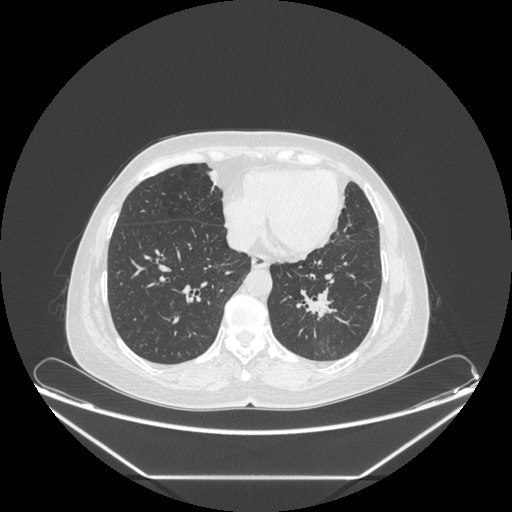
Chest CT, one axial slice; slice 82 of 241 in the series (ordered by position); reconstruction kernel STANDARD; lung window (W 1500 / L -600 HU); 512 × 512 image matrix, field of view 451 × 451 mm. Patient: female, 63 years. From the clinical record (not read from this slice): clinical TNM (as recorded): T1c N0 M0.
Annotated regions visible in this slice (bounding box drawn by a radiologist):
- lung tumour (recorded histology: adenocarcinoma): bounding box [x1, y1, x2, y2] px = [295, 283, 343, 328]